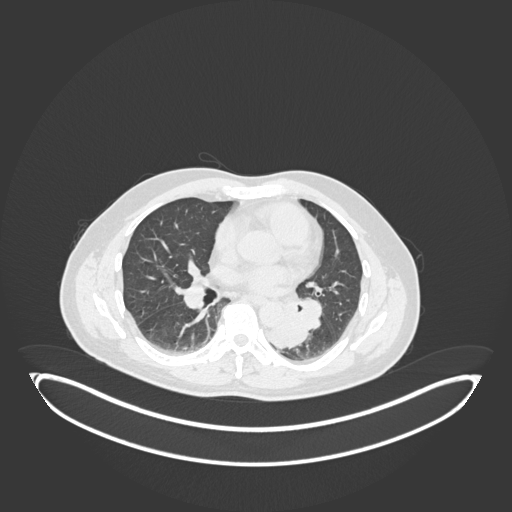
Chest CT, one axial slice. Reconstruction kernel B30f. 120 kVp. Lung window (W 1500 / L -600 HU). 1 mm slice thickness. 512 × 512 image matrix. Male patient, age 54 years. From the clinical record (not read from this slice): clinical TNM (as recorded): T3 N0 M0.
Annotated regions visible in this slice (bounding box drawn by a radiologist):
- lung tumour (recorded histology: squamous cell carcinoma): box from (x=263, y=300) to (x=311, y=348) px